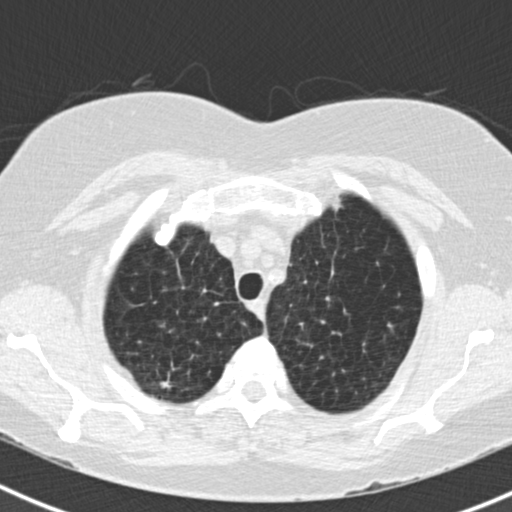
Low-dose screening chest CT, one axial slice; slice 146 of 180 in the series (ordered by position); reconstruction kernel B30f; lung window (W 1500 / L -600 HU); 512 × 512 image matrix, field of view 310 × 310 mm.
Annotated regions visible in this slice (expert manual segmentation):
- lesion 1 (tumor, upper lobe of right lung): bounding box [x1, y1, x2, y2] px = [160, 380, 171, 388]